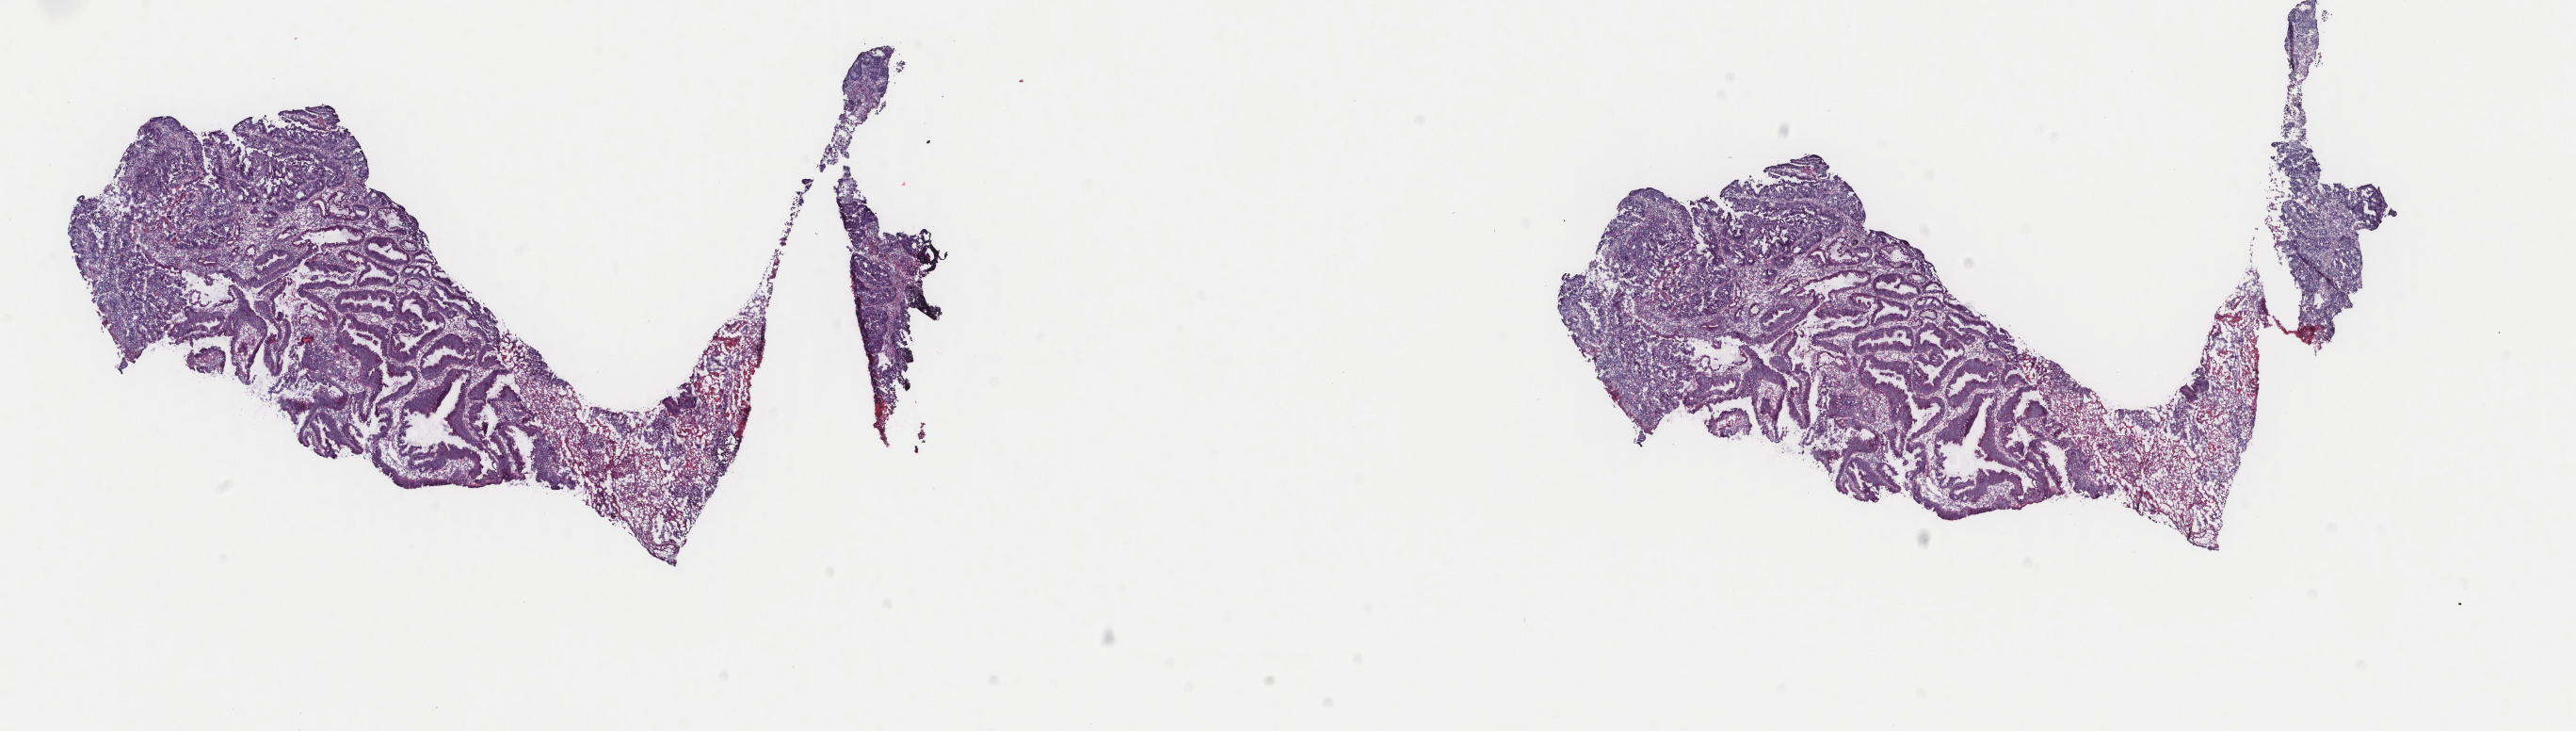
Whole-slide histology image, H&E-stained — a low-resolution overview of the entire scanned area, about 21.7 x 6.2 mm (acquisition: 40x scan); frozen section from the top of the tissue portion; primary tumour sample from the colon. Female patient; age at initial diagnosis 74 years. Slide review estimates, as recorded: tumour cells 60%, tumour nuclei 75%, normal cells 0%, stromal cells 20%, necrosis 20%. Infiltration values recorded for this section: lymphocyte infiltration 10%, monocyte infiltration 3%, neutrophil infiltration 3%.
* histologic diagnosis: Adenocarcinoma, NOS (hepatic flexure of colon)
* lymph nodes positive (case pathology): 0 of 24 examined
* AJCC pathologic stage: I (7th edition)
* TNM: T2 N0 M0